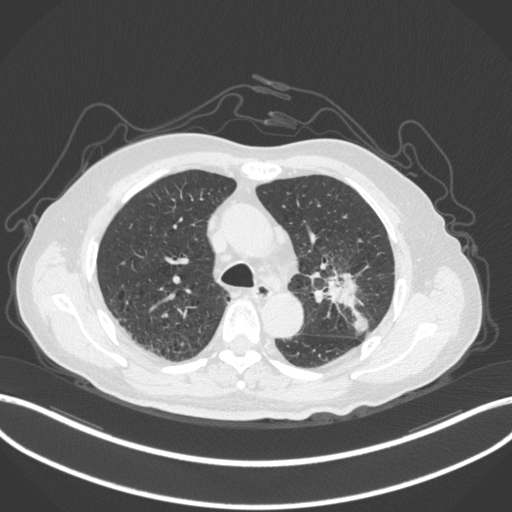
Chest CT, one axial slice; position 194 of 331 along the scan axis; lung window (W 1500 / L -600 HU); 512 × 512 image matrix, field of view 400 × 400 mm. Male patient, age 79 years. From the clinical record (not read from this slice): clinical TNM (as recorded): T2a N1 M1.
Annotated regions visible in this slice (rectangle marked by the reading radiologist):
- lung tumour (recorded histology: adenocarcinoma): bounding box <323,267,368,332> (left, top, right, bottom; pixels)